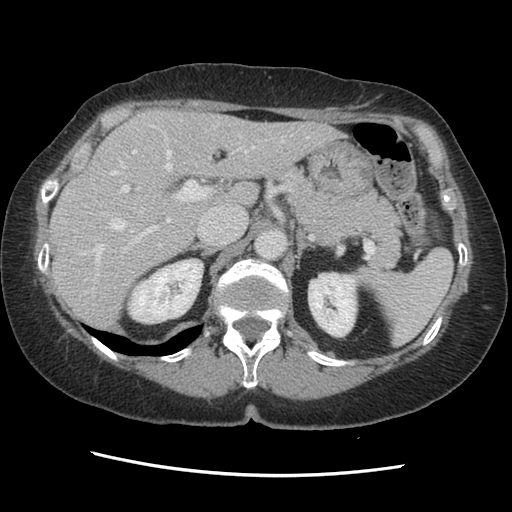
Contrast-enhanced abdominal CT, one axial slice; position 90 of 141 along the scan axis; soft-tissue window (W 400 / L 40 HU); 512 × 512 image matrix, field of view 330 × 330 mm. Female patient, age 61 years. Case-level facts recorded for this patient, not image findings: diagnosis: colorectal cancer liver metastases, imaged before liver resection; multiple liver metastases: no; largest metastasis: 2.4 cm.
Outlined on this slice (outlined manually by an expert reader):
- hepatic veins: bounding box <85,125,309,292> (left, top, right, bottom; pixels)
- liver: <51,110,339,331>
- planned liver remnant (the part of the liver to remain after resection): <51,110,339,332>
- portal vein (with intrahepatic branches): <120,148,242,253>